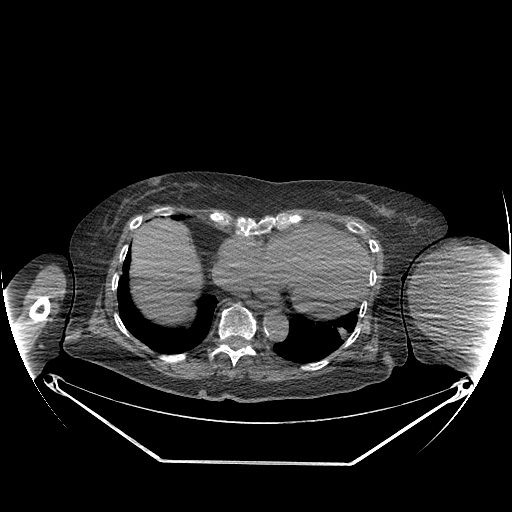
CT of an extremity soft-tissue mass (from a PET/CT study), one axial slice; slice 151 of 267 in the series (ordered by position); soft-tissue window (W 400 / L 40 HU); 3.75 mm slice thickness; 512 × 512 image matrix, field of view 500 × 500 mm. Female patient. Case-level facts recorded for this patient, not image findings: histological type: pleiomorphic leiomyosarcoma; grade: high; site of the primary tumour: left biceps.
Outlined on this slice (expert contour drawn on MRI and transferred to this co-registered scan by the dataset authors):
- gross tumour volume including surrounding oedema: bounding box (x1, y1, x2, y2) in pixels: (411, 247, 497, 327)
- gross tumour volume (mass): (411, 247, 497, 327)